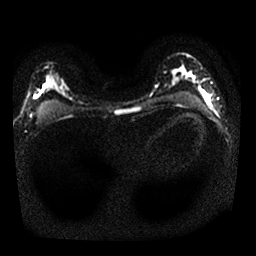
Breast MRI, one axial slice; slice 15 of 25 in the series (ordered by position); diffusion-weighted series; image 2 of 4 stored at this slice position (different b-values; order by instance number); 1.5 T; 256 × 256 image matrix, field of view 320 × 320 mm. Female patient.
Outlined on this slice (outlined manually by an expert reader):
- tumour on diffusion-weighted imaging: bounding box [x1, y1, x2, y2] px = [203, 93, 207, 98]